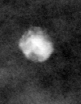
Cropped region of a digitized screen-film mammogram centred on a radiologist-marked abnormality; right breast; CC view; BI-RADS breast density category 2 (scale 1–4).
- Calcifications, morphology coarse / round and regular / lucent center; BI-RADS assessment category 2; benign without callback (not worked up further).